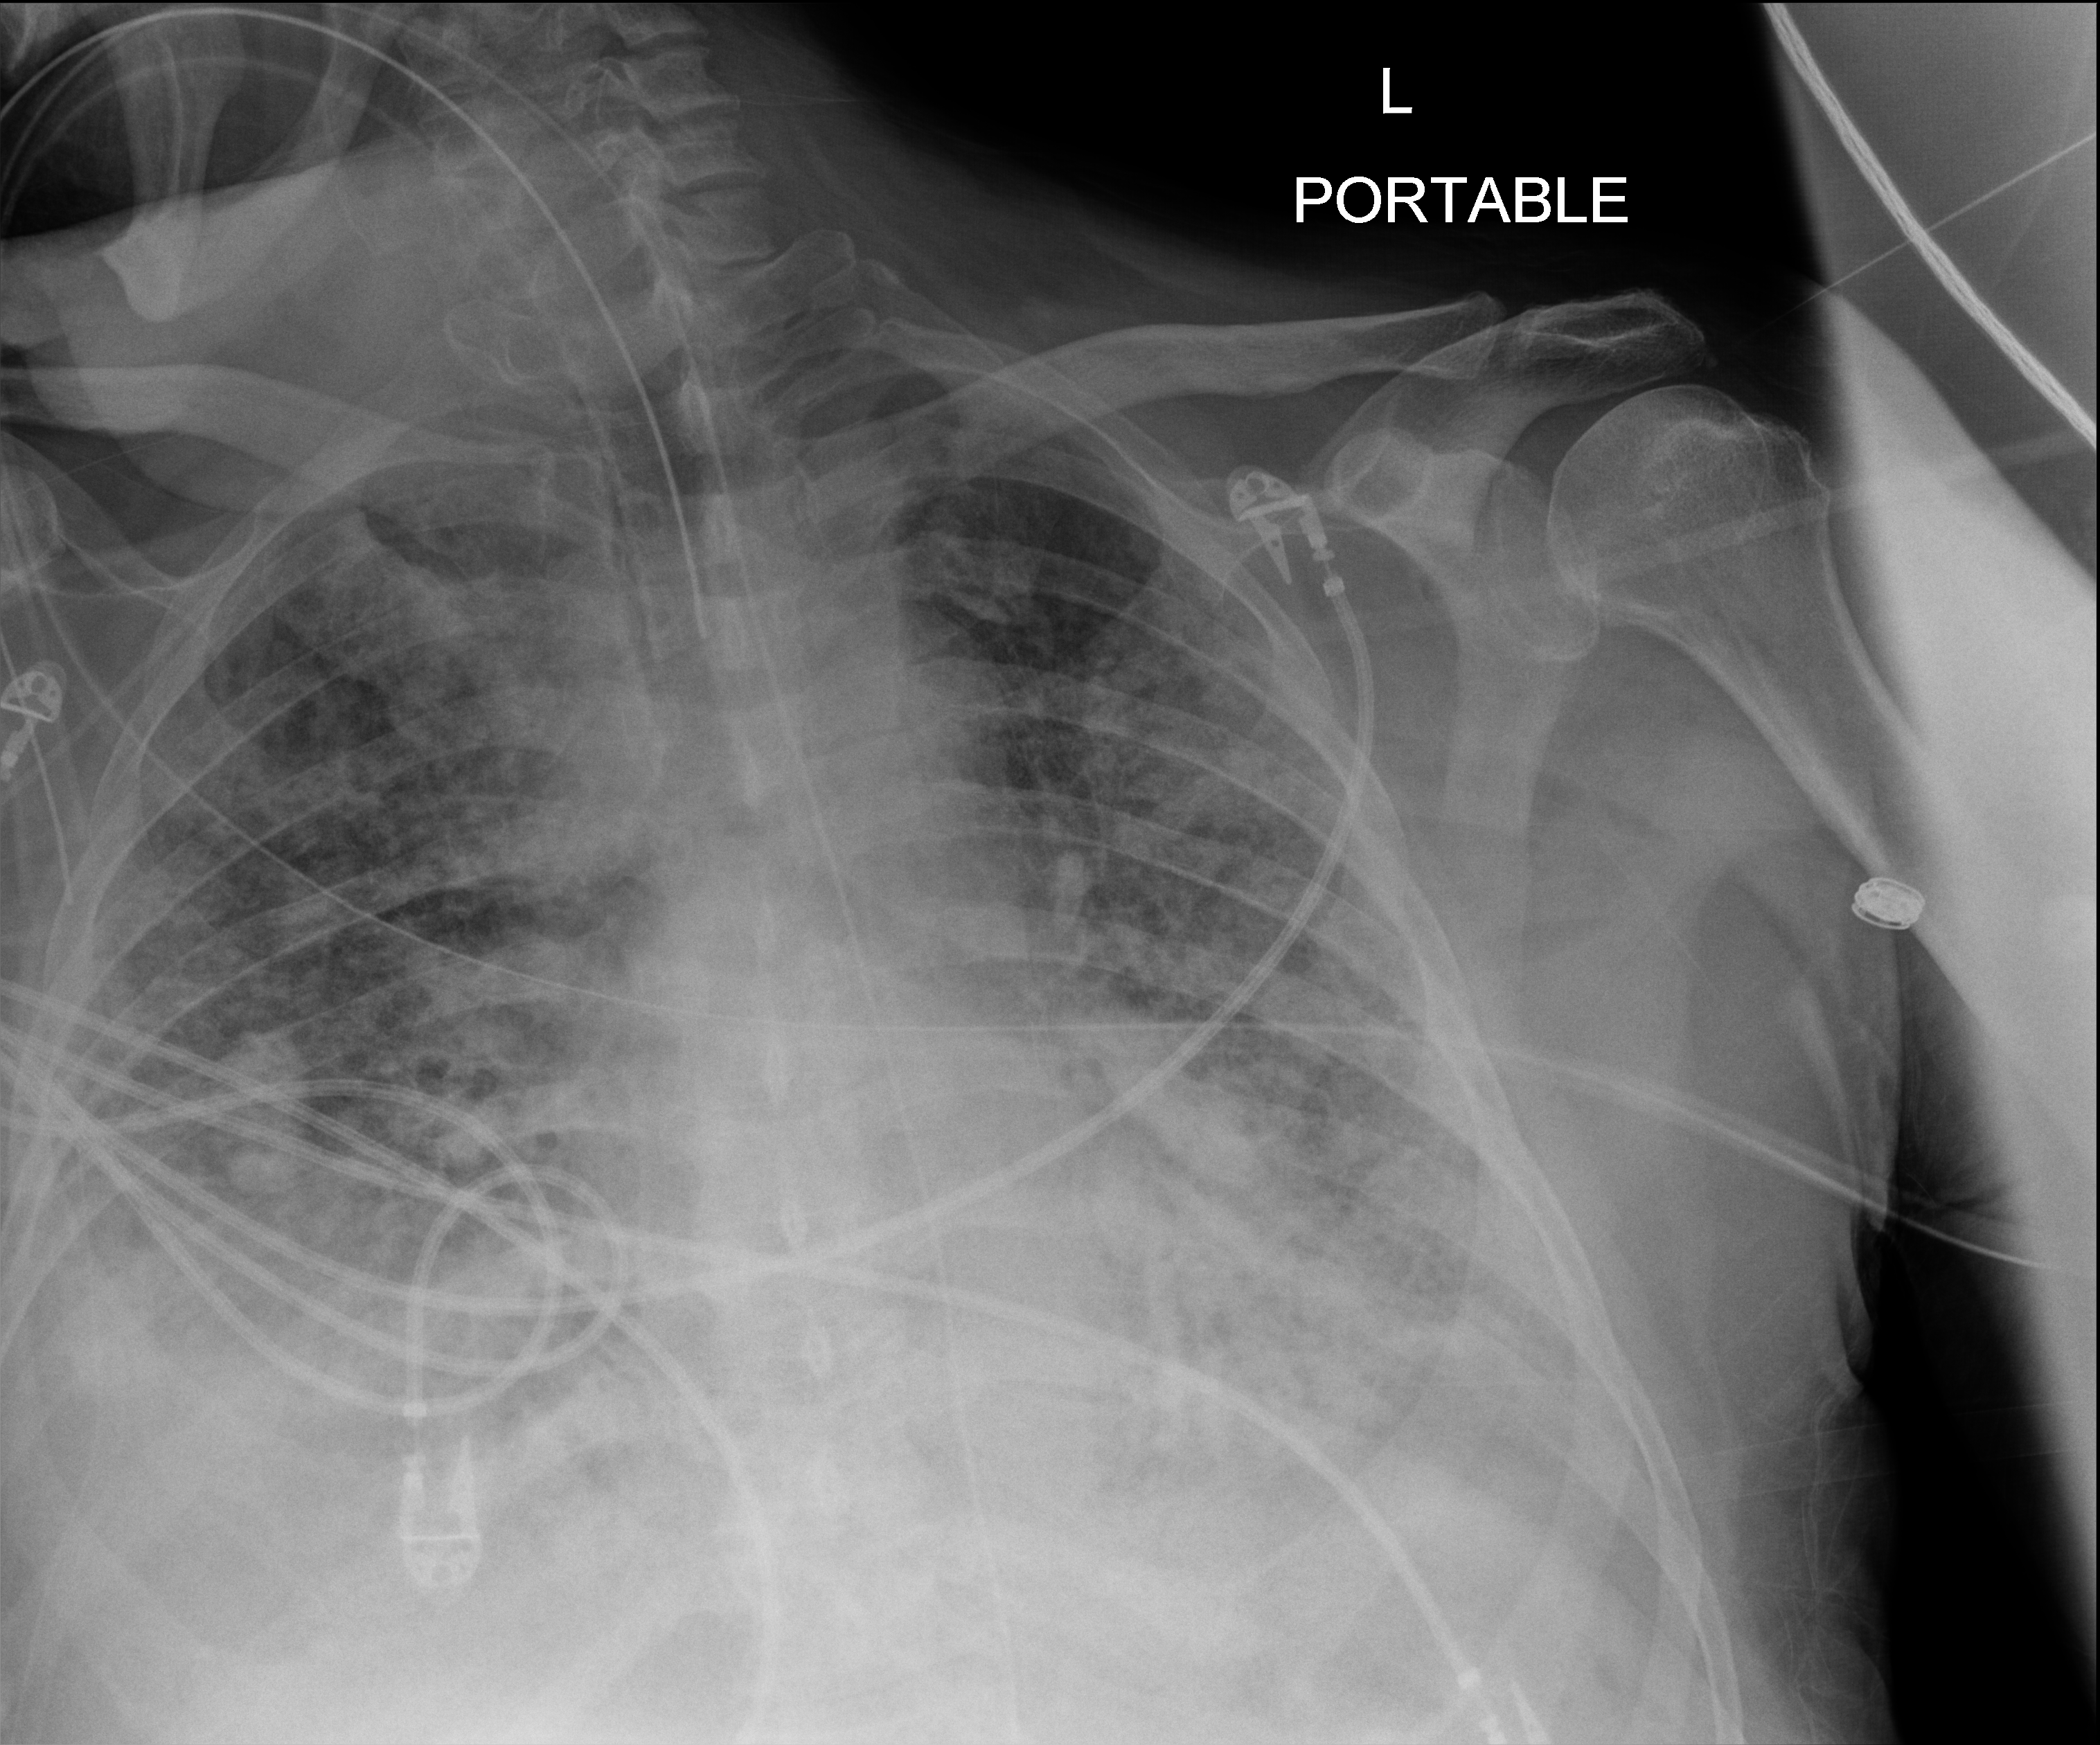
Chest X-ray (portable); anteroposterior (AP) projection. Male patient hospitalised with COVID-19, age 60–74 years.
From the hospital-stay record, not from the radiograph (when in the stay this image was taken is not recorded):
- admitted to intensive care during this hospital stay: yes
- length of hospital stay: 26 days
- mechanically ventilated during this hospital stay: yes